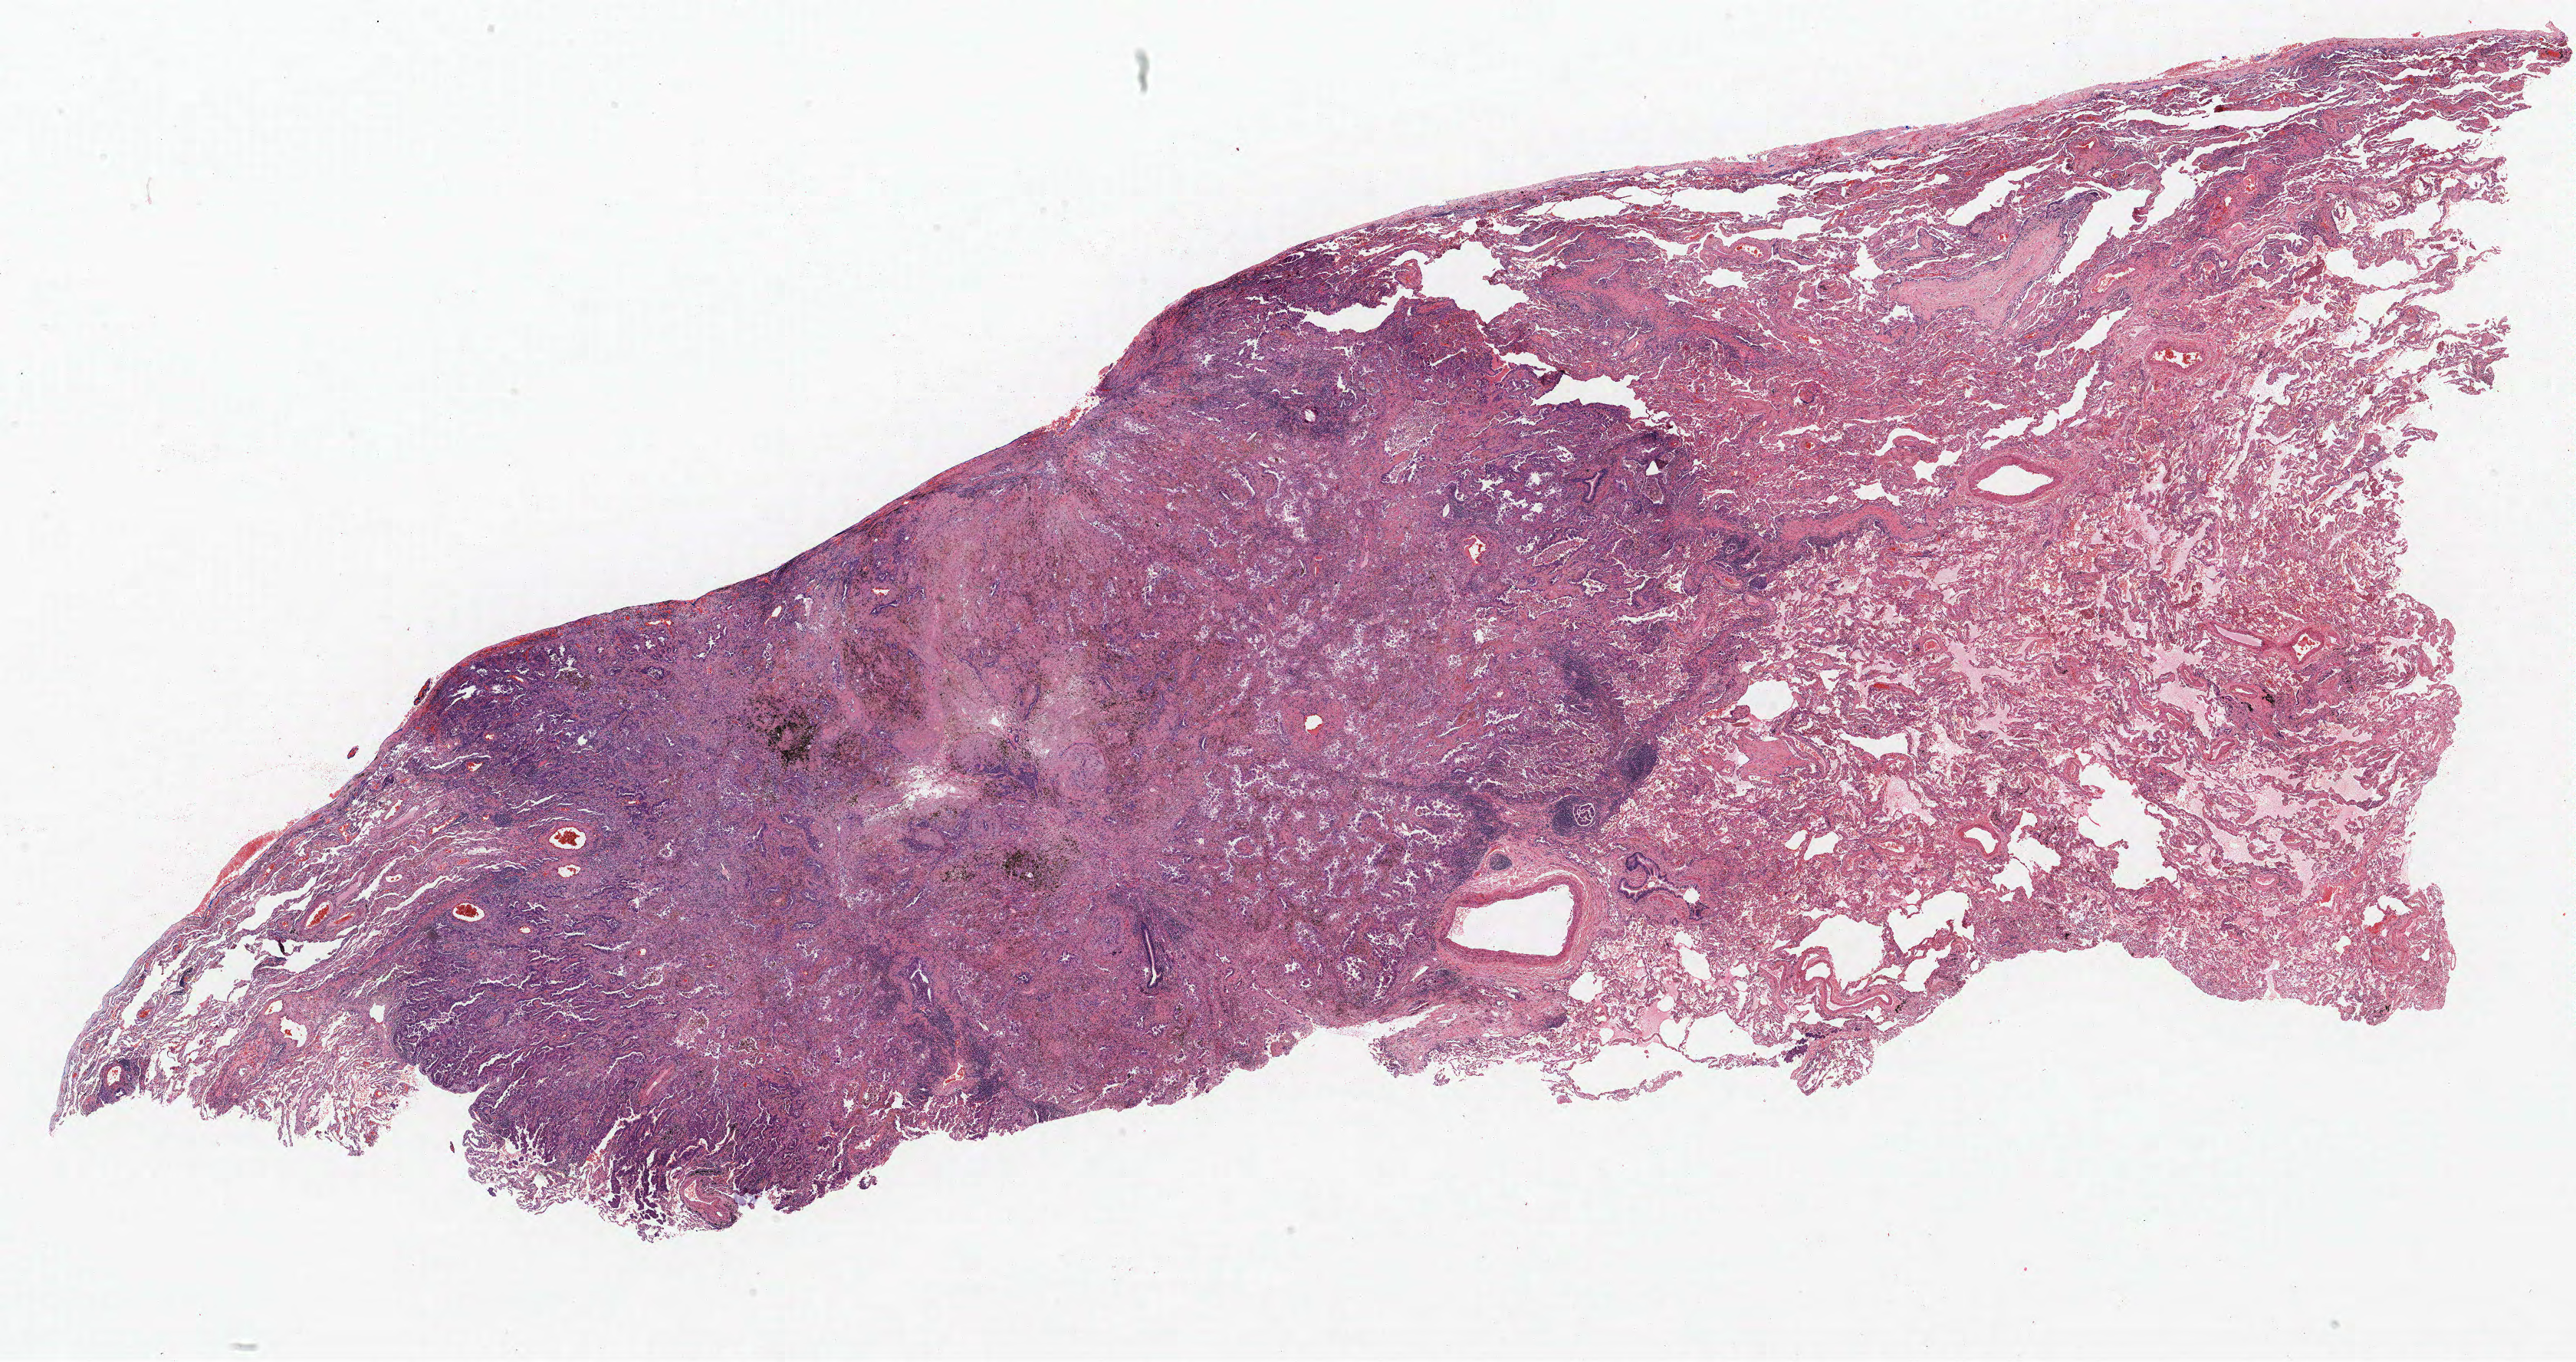
Whole-slide histology image, Hematoxylin and eosin (H&E) stained — low-resolution overview of the scanned area, about 26.9 x 14.2 mm (acquisition: 40x scan). Formalin-fixed paraffin-embedded (FFPE) section. Lung tissue. Male patient, aged 70 at enrolment. Grade: poorly differentiated (G3).
Primary tumour location (clinical record): left upper lobe. Stage (AJCC 6th edition): IIB. Participant's lung-cancer diagnosis: Mixed cell adenocarcinoma. Tumour size (pathology): 17 mm.